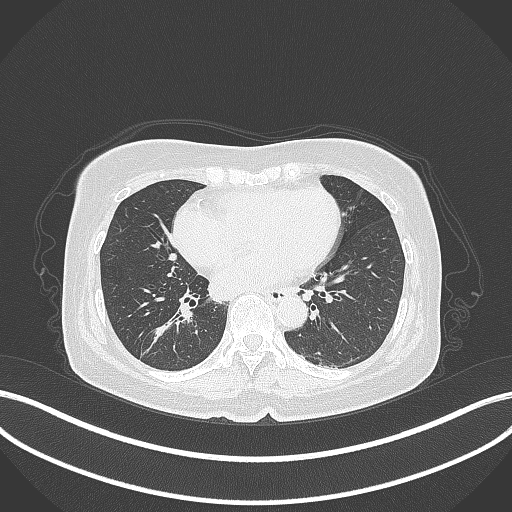
Chest CT, one axial slice; slice 167 of 429 in the series (ordered by position); reconstruction kernel B70f; 120 kVp; lung window (W 1500 / L -600 HU); 1 mm slice thickness; 512 × 512 image matrix, field of view 400 × 400 mm. Patient: female, 67 years. From the clinical record (not read from this slice): clinical TNM (as recorded): T1c N1 M0.
Annotated regions visible in this slice (bounding box drawn by a radiologist):
- lung tumour (recorded histology: adenocarcinoma): box from (x=140, y=302) to (x=198, y=361) px